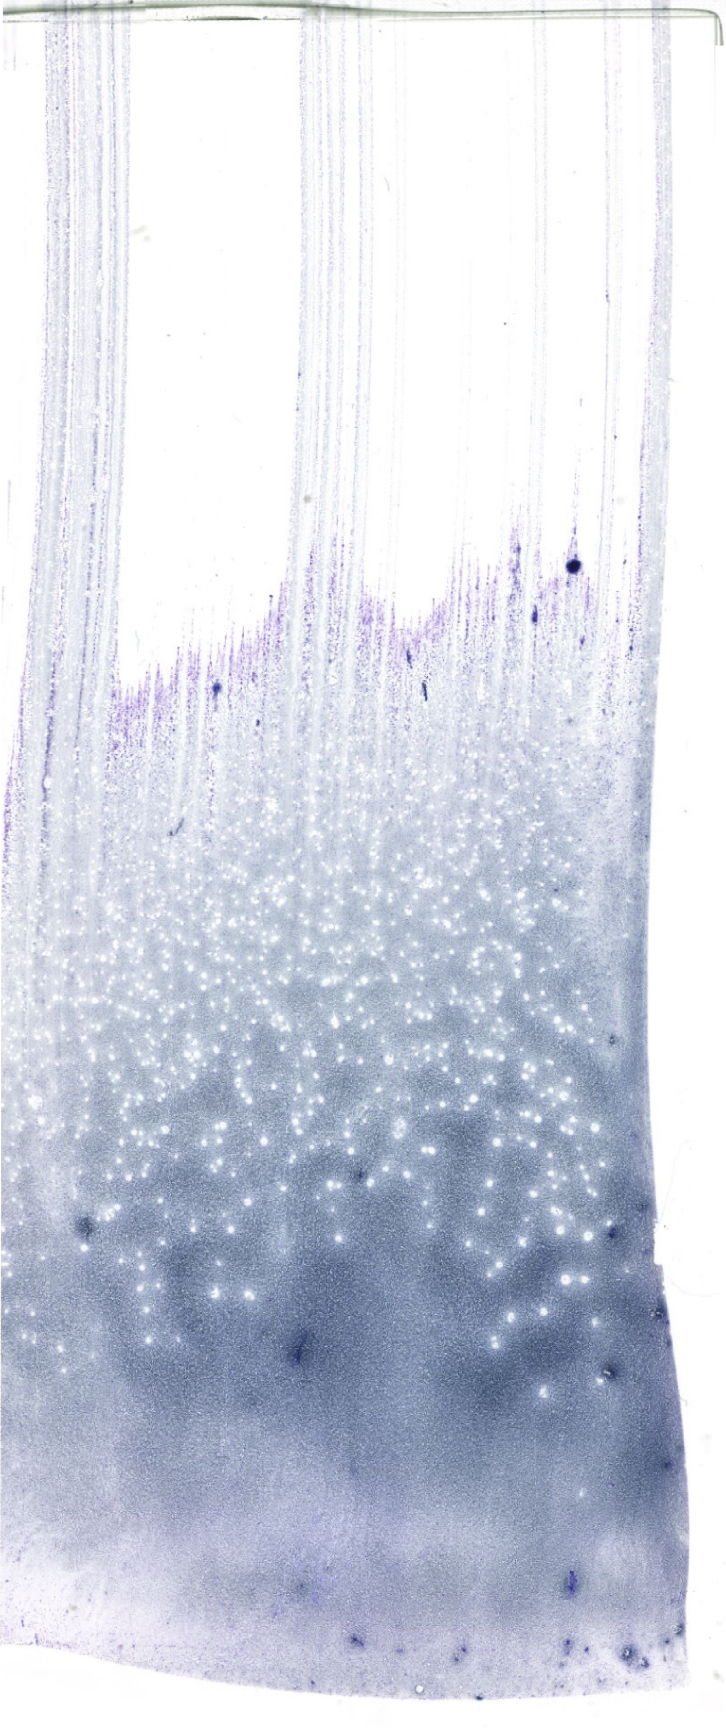
Bone marrow aspirate smear, May-Grünwald–Giemsa stain, whole-slide image, low-resolution overview of the scanned area, about 20.6 x 49.0 mm. Patient sex: male.
Diagnosis: B Acute Lymphoblastic Leukemia.